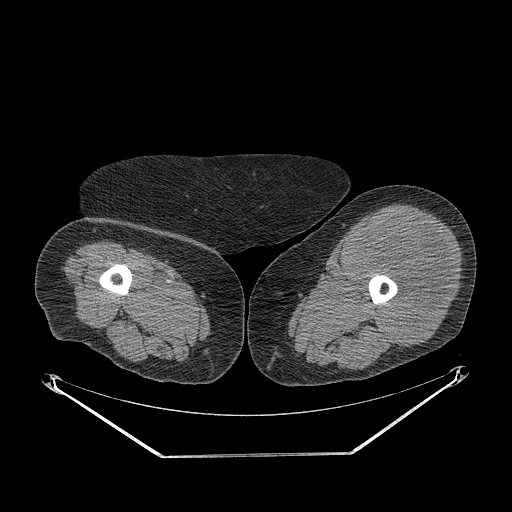
CT of an extremity soft-tissue mass (from a PET/CT study), one axial slice; slice 230 of 267 in the series (ordered by position); reconstruction kernel STANDARD; soft-tissue window (W 400 / L 40 HU); 3.75 mm slice thickness; 512 × 512 image matrix, field of view 500 × 500 mm. Female patient. Case-level facts recorded for this patient, not image findings: histological type: undifferentiated – high grade; grade: high; site of the primary tumour: left thigh.
Annotated regions visible in this slice (expert contour drawn on MRI and transferred to this co-registered scan by the dataset authors):
- gross tumour volume including surrounding oedema: bounding box [x1, y1, x2, y2] px = [354, 215, 453, 346]
- gross tumour volume (mass): [354, 215, 451, 346]